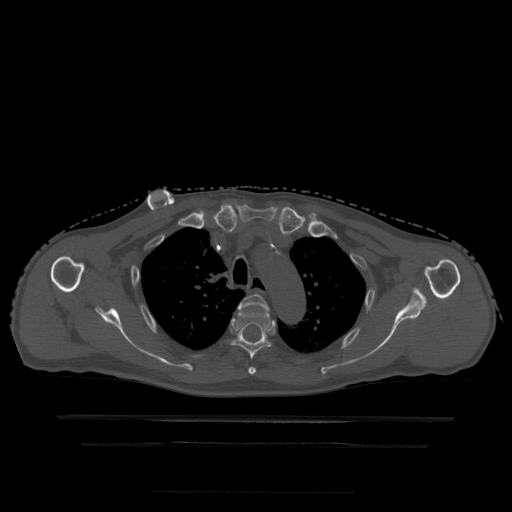
CT including the spine, one axial slice; position 357 of 522 along the scan axis; bone window (W 1800 / L 400 HU); 1.25 mm slice thickness; 512 × 512 image matrix, field of view 436 × 436 mm. Patient age 68 years. Case-level facts recorded for this patient, not image findings: primary cancer: urothelial.
Outlined on this slice (semi-automatically segmented with operator editing):
- T3 vertebra: bounding box <238,295,269,374> (left, top, right, bottom; pixels)
- T4 vertebra: <232,308,274,375>